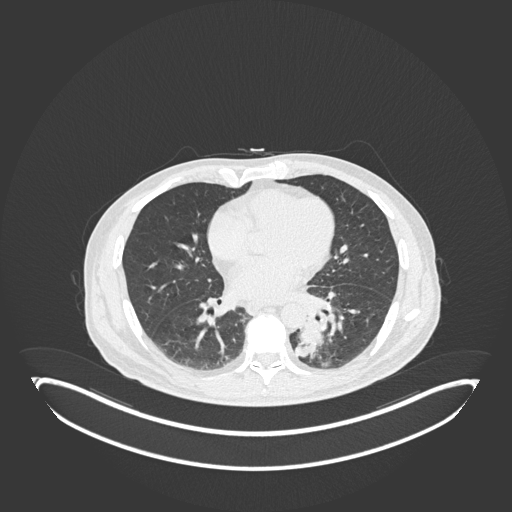
Chest CT, one axial slice; position 73 of 251 along the scan axis; 120 kVp; lung window (W 1500 / L -600 HU); 1 mm slice thickness; 512 × 512 image matrix, field of view 500 × 500 mm. Male patient, age 72 years. From the clinical record (not read from this slice): clinical TNM (as recorded): T2b N0 M1.
Outlined on this slice (rectangle marked by the reading radiologist):
- lung tumour (recorded histology: adenocarcinoma): box from (x=295, y=319) to (x=324, y=358) px